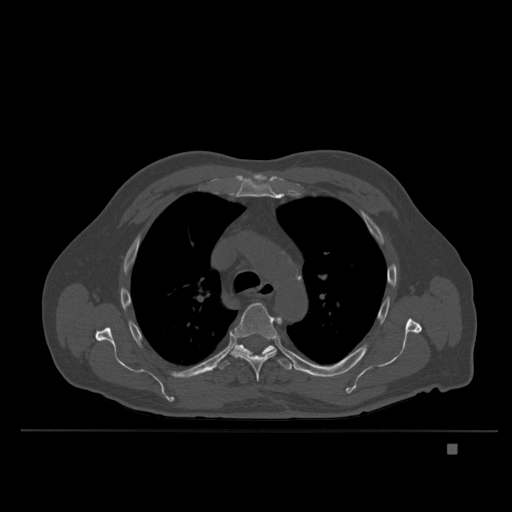
CT including the spine, one axial slice. Slice 270 of 435 in the series (ordered by position). Bone window (W 1800 / L 400 HU). 1.5 mm slice thickness. 512 × 512 image matrix, field of view 434 × 434 mm. Male patient, age 73 years. Case-level facts recorded for this patient, not image findings: primary cancer: skin.
Structures marked on this image (semi-automatic segmentation, software-assisted and operator-edited):
- T5 vertebra: bounding box [x1, y1, x2, y2] px = [230, 303, 282, 382]
- T6 vertebra: [218, 344, 292, 370]